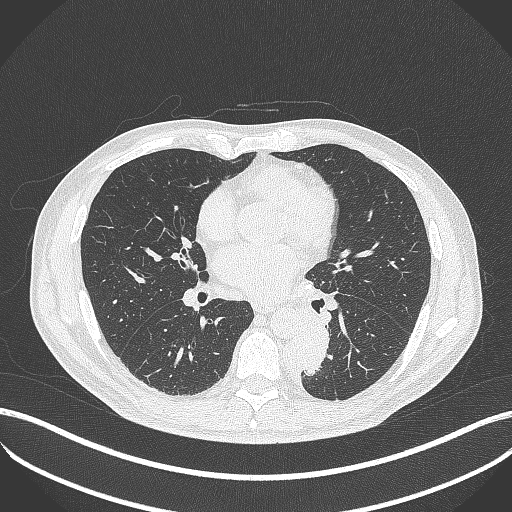
Chest CT, one axial slice; slice 199 of 451 in the series (ordered by position); reconstruction kernel B70f; 120 kVp; lung window (W 1500 / L -600 HU); 1 mm slice thickness; 512 × 512 image matrix, field of view 400 × 400 mm. Male patient, age 72 years. Case-level facts recorded for this patient, not image findings: clinical TNM (as recorded): T2b N0 M1.
Structures marked on this image (bounding box drawn by a radiologist):
- lung tumour (recorded histology: adenocarcinoma): bounding box <291,317,331,381> (left, top, right, bottom; pixels)